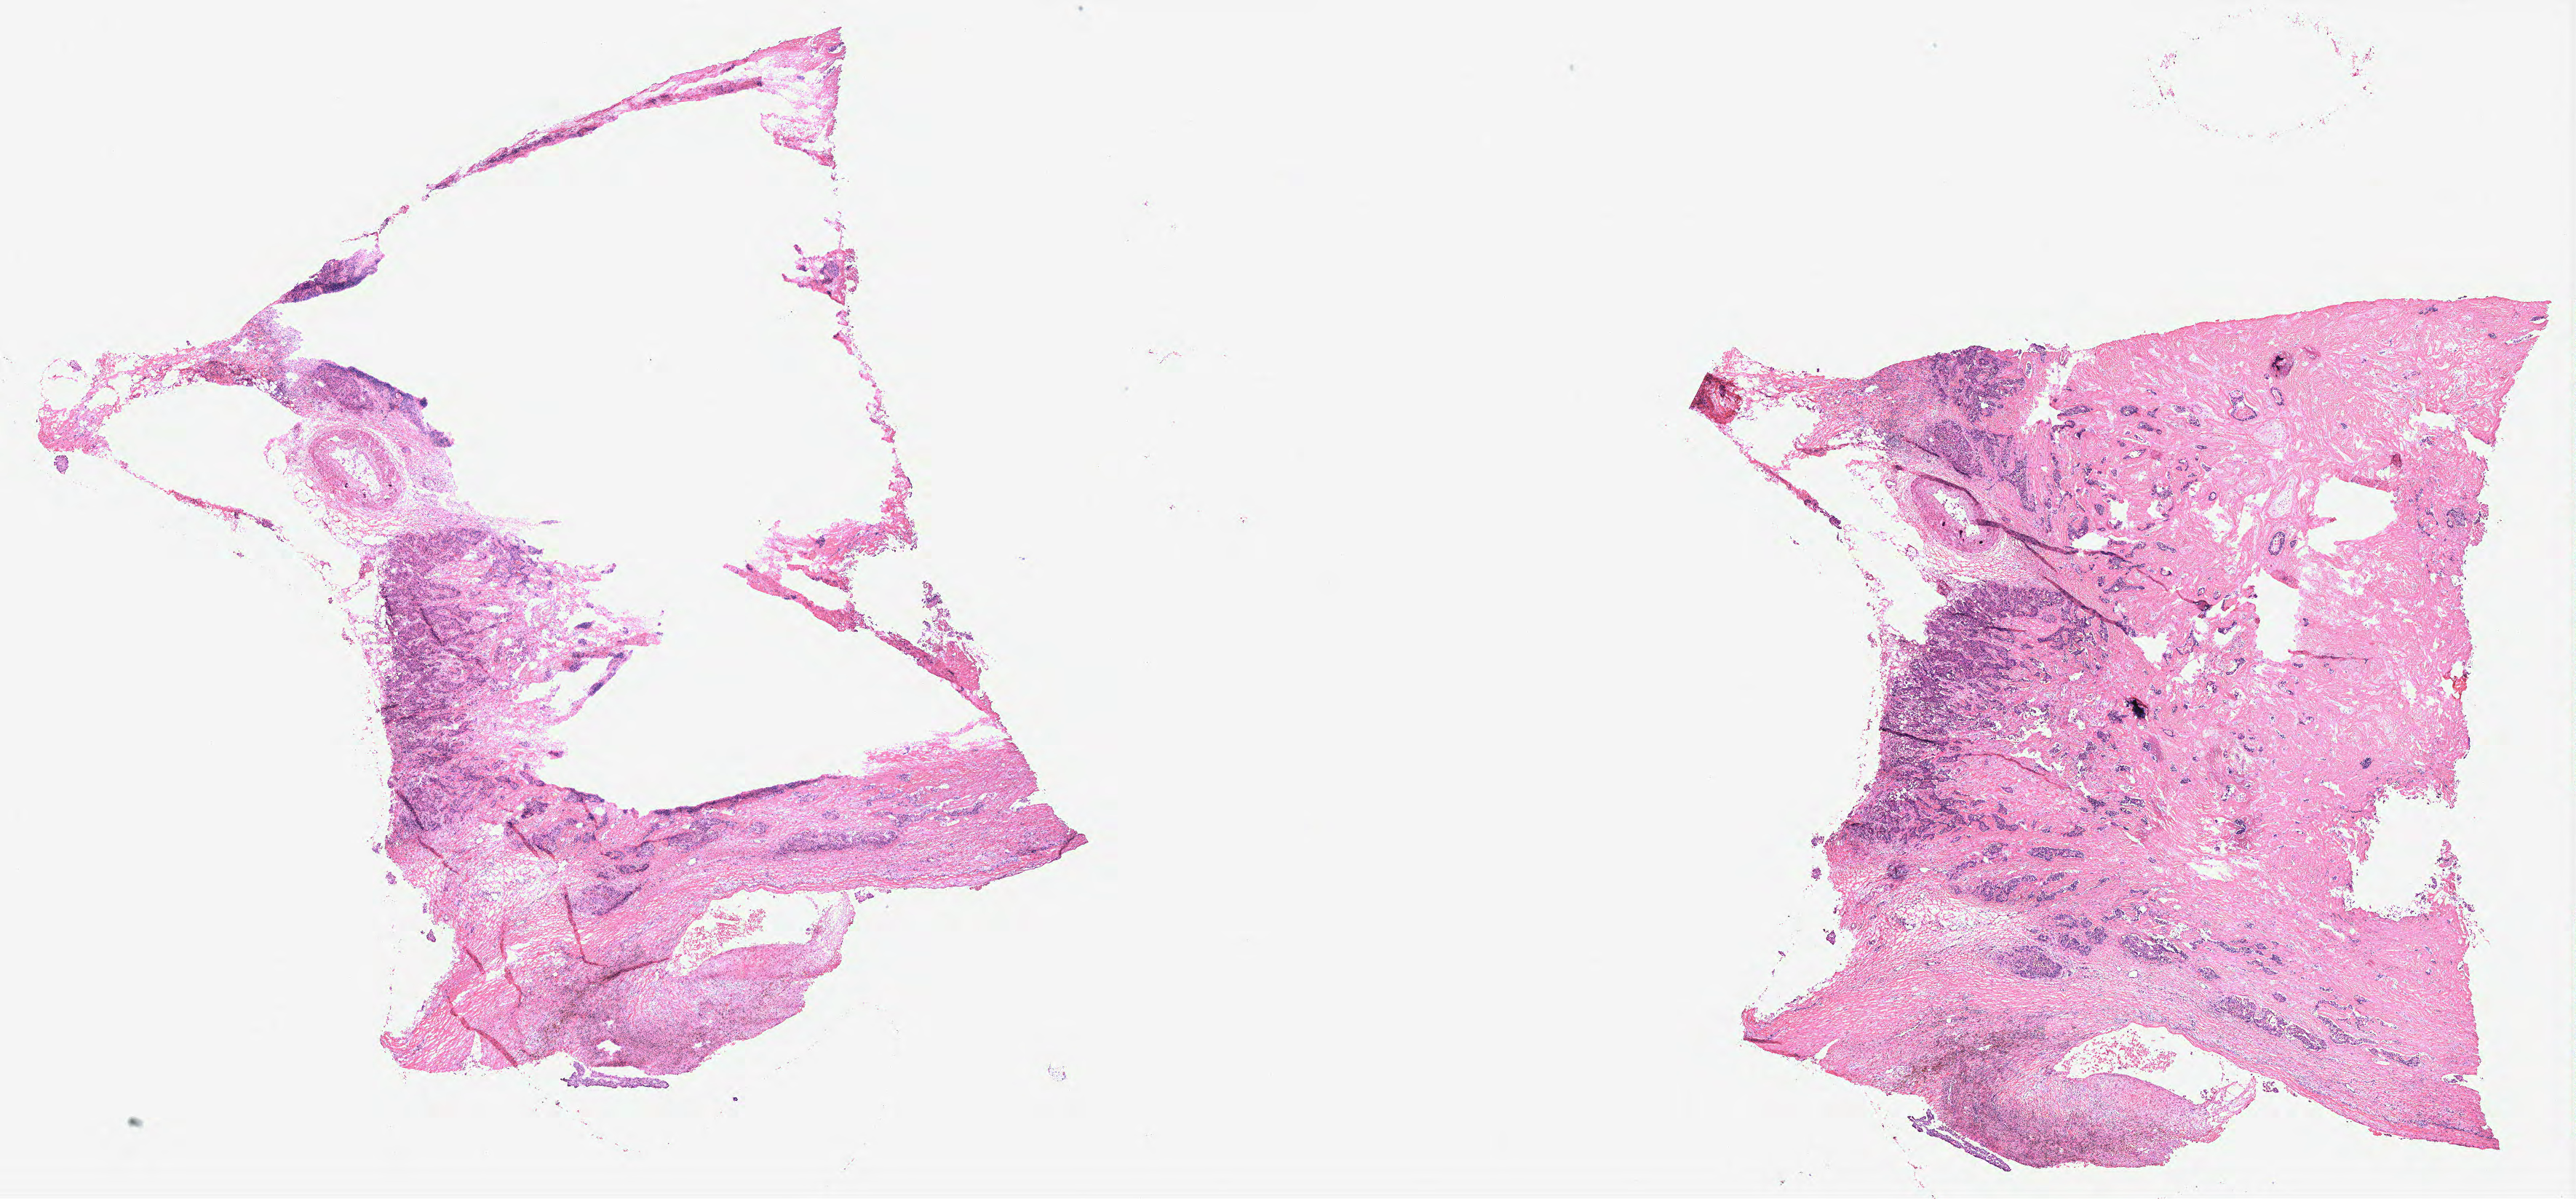
Digitized H&E tissue section (whole slide) — shown as a low-resolution overview of the whole scanned area (about 28.3 x 13.2 mm, from a 40x scan); breast, tissue type not recorded. 71-year-old female patient.
Patient diagnosis: Intraductal papillary carcinoma.